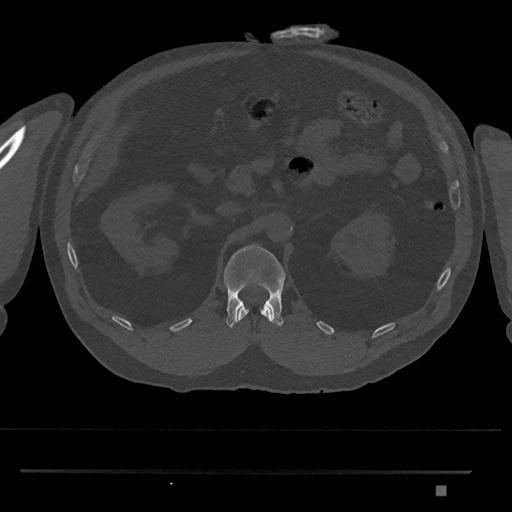
CT including the spine, one axial slice; position 844 of 1134 along the scan axis; reconstruction kernel Br40s/3; 120 kVp; bone window (W 1800 / L 400 HU); 512 × 512 image matrix. Male patient, age 65 years. Case-level facts recorded for this patient, not image findings: primary cancer: prostate.
Outlined on this slice (semi-automatically segmented with operator editing):
- L1 vertebra: bounding box [x1, y1, x2, y2] px = [223, 244, 286, 328]
- T12 vertebra: [237, 305, 272, 322]